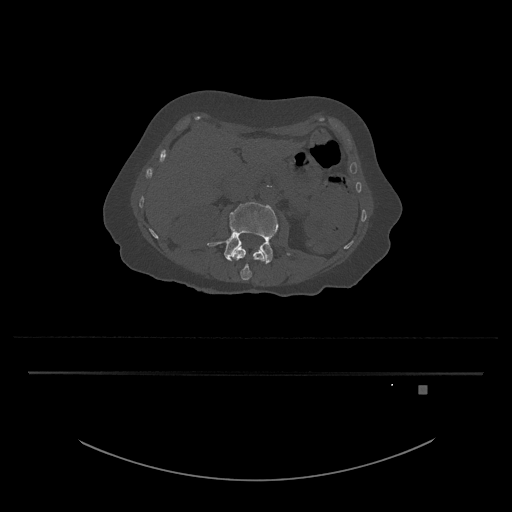
CT including the spine, one axial slice. Position 453 of 797 along the scan axis. Reconstruction kernel Br40s/3. Bone window (W 1800 / L 400 HU). 512 × 512 image matrix, field of view 500 × 500 mm. Patient: female, 57 years. Case-level facts recorded for this patient, not image findings: primary cancer: cervical.
Structures marked on this image (semi-automatically segmented with operator editing):
- L3 vertebra: bounding box [x1, y1, x2, y2] px = [207, 202, 291, 264]